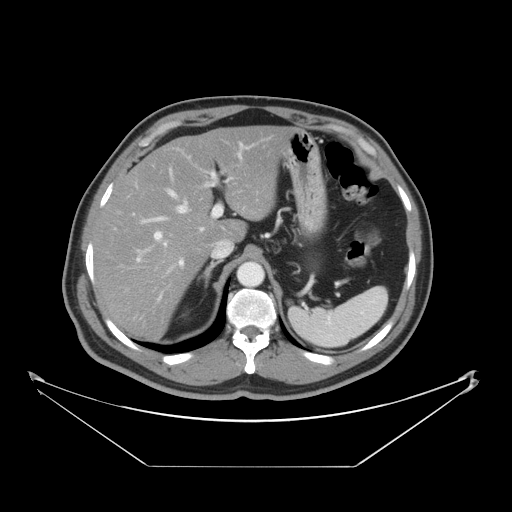
Contrast-enhanced abdominal CT, one axial slice. Slice 31 of 46 in the series (ordered by position). 120 kVp. Intravenous contrast given. Soft-tissue window (W 400 / L 40 HU). 5 mm slice thickness. 512 × 512 image matrix. Male patient, age 57 years. Case-level facts recorded for this patient, not image findings: diagnosis: colorectal cancer liver metastases, imaged before liver resection; multiple liver metastases: no; largest metastasis: 3.3 cm; disease in both lobes: no.
Annotated regions visible in this slice (outlined manually by an expert reader):
- hepatic veins: box from (x=141, y=188) to (x=190, y=224) px
- liver: (x=92, y=127)–(x=289, y=339)
- planned liver remnant (the part of the liver to remain after resection): (x=92, y=127)–(x=289, y=336)
- portal vein (with intrahepatic branches): (x=135, y=153)–(x=241, y=301)